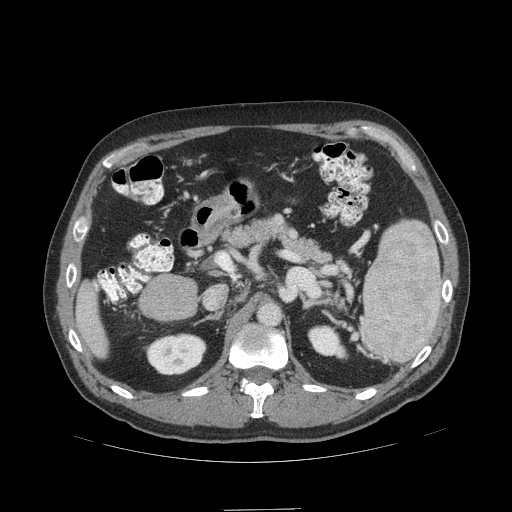
Contrast-enhanced abdominal CT (liver protocol), one axial slice; position 58 of 99 along the scan axis; soft-tissue window (W 400 / L 40 HU); 2.5 mm slice thickness; 512 × 512 image matrix. Case-level facts recorded for this patient, not image findings: diagnosis: hepatocellular carcinoma (patient treated with transarterial chemoembolisation; whether this scan precedes or follows treatment is not stated here); TNM stage (as recorded): Stage-I; Child-Pugh class: A; tumour differentiation: no biopsy; tumour nodularity: uninodular.
Structures marked on this image (semi-automatically segmented with operator editing):
- liver parenchyma outside the tumour (the mass and vessels are separate outlines, so this box may not span the whole liver): bounding box (x1, y1, x2, y2) in pixels: (76, 280, 108, 358)
- liver vessels: (95, 284, 97, 287)